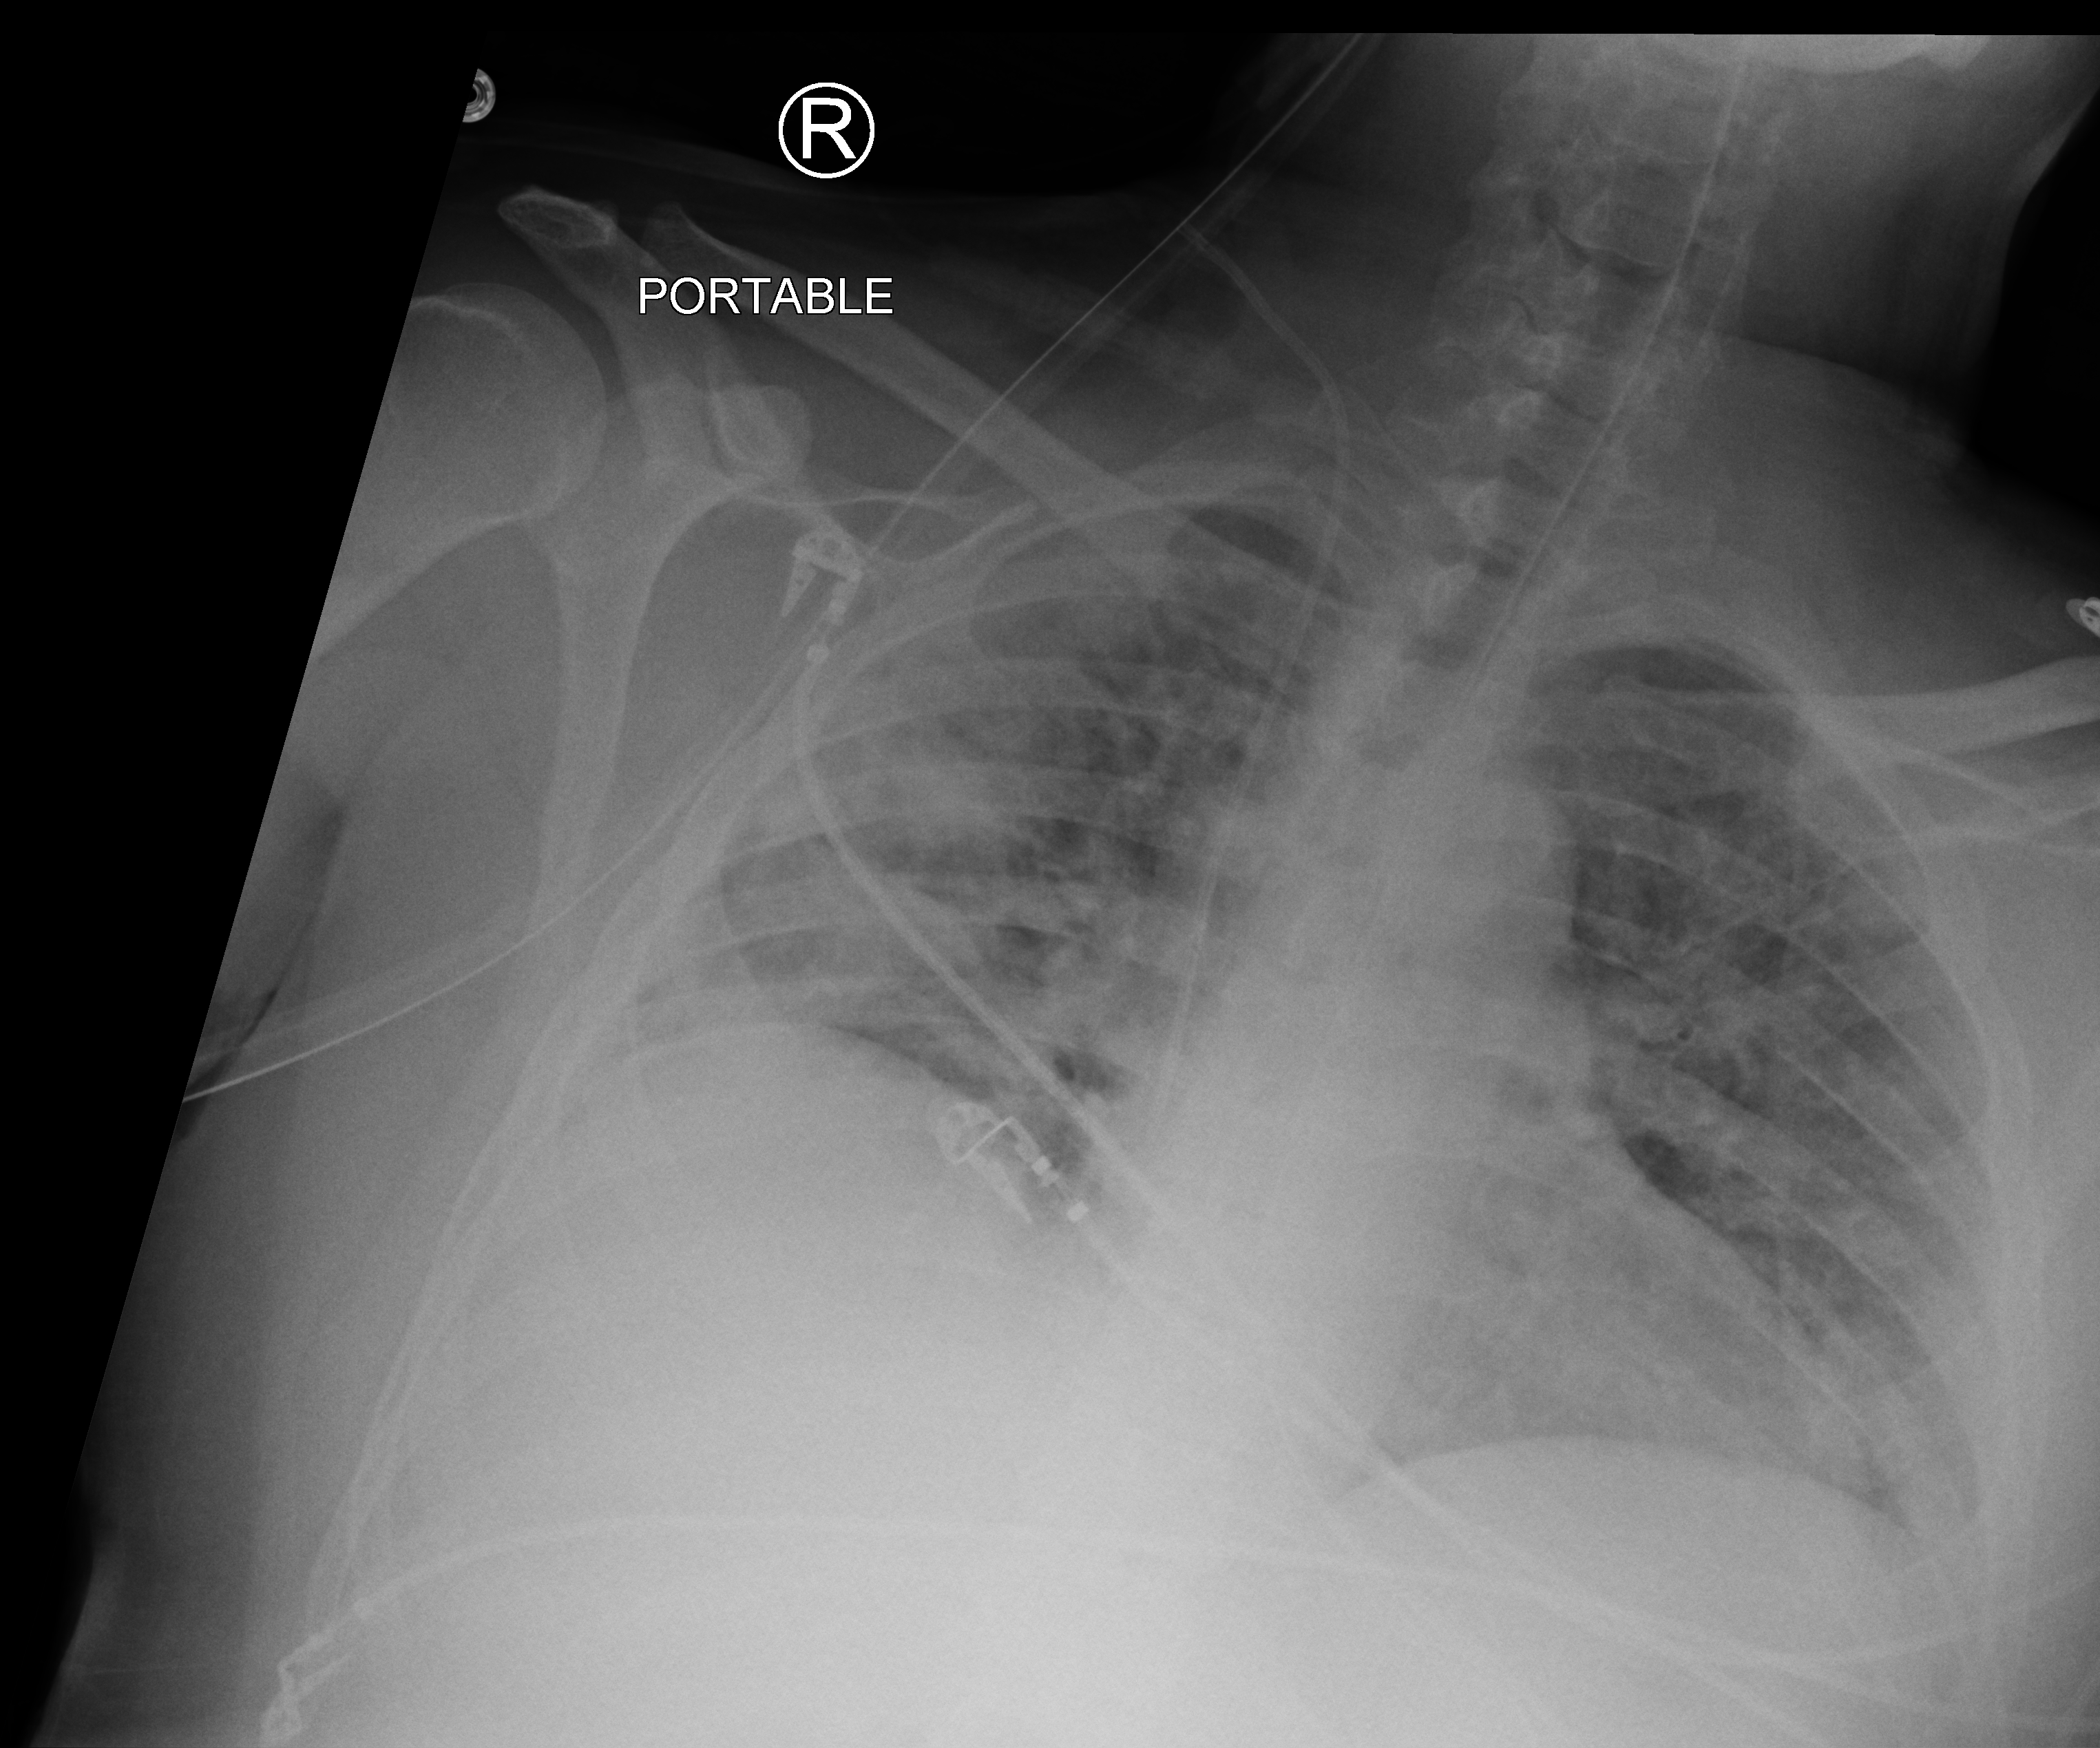
Portable chest radiograph; anteroposterior (AP) projection. Male patient hospitalised with COVID-19, age 18–59 years.
Hospital-stay facts (about this admission, not read from this image; timing relative to this image not recorded): admitted to intensive care during this hospital stay: yes; length of hospital stay: 22 days.